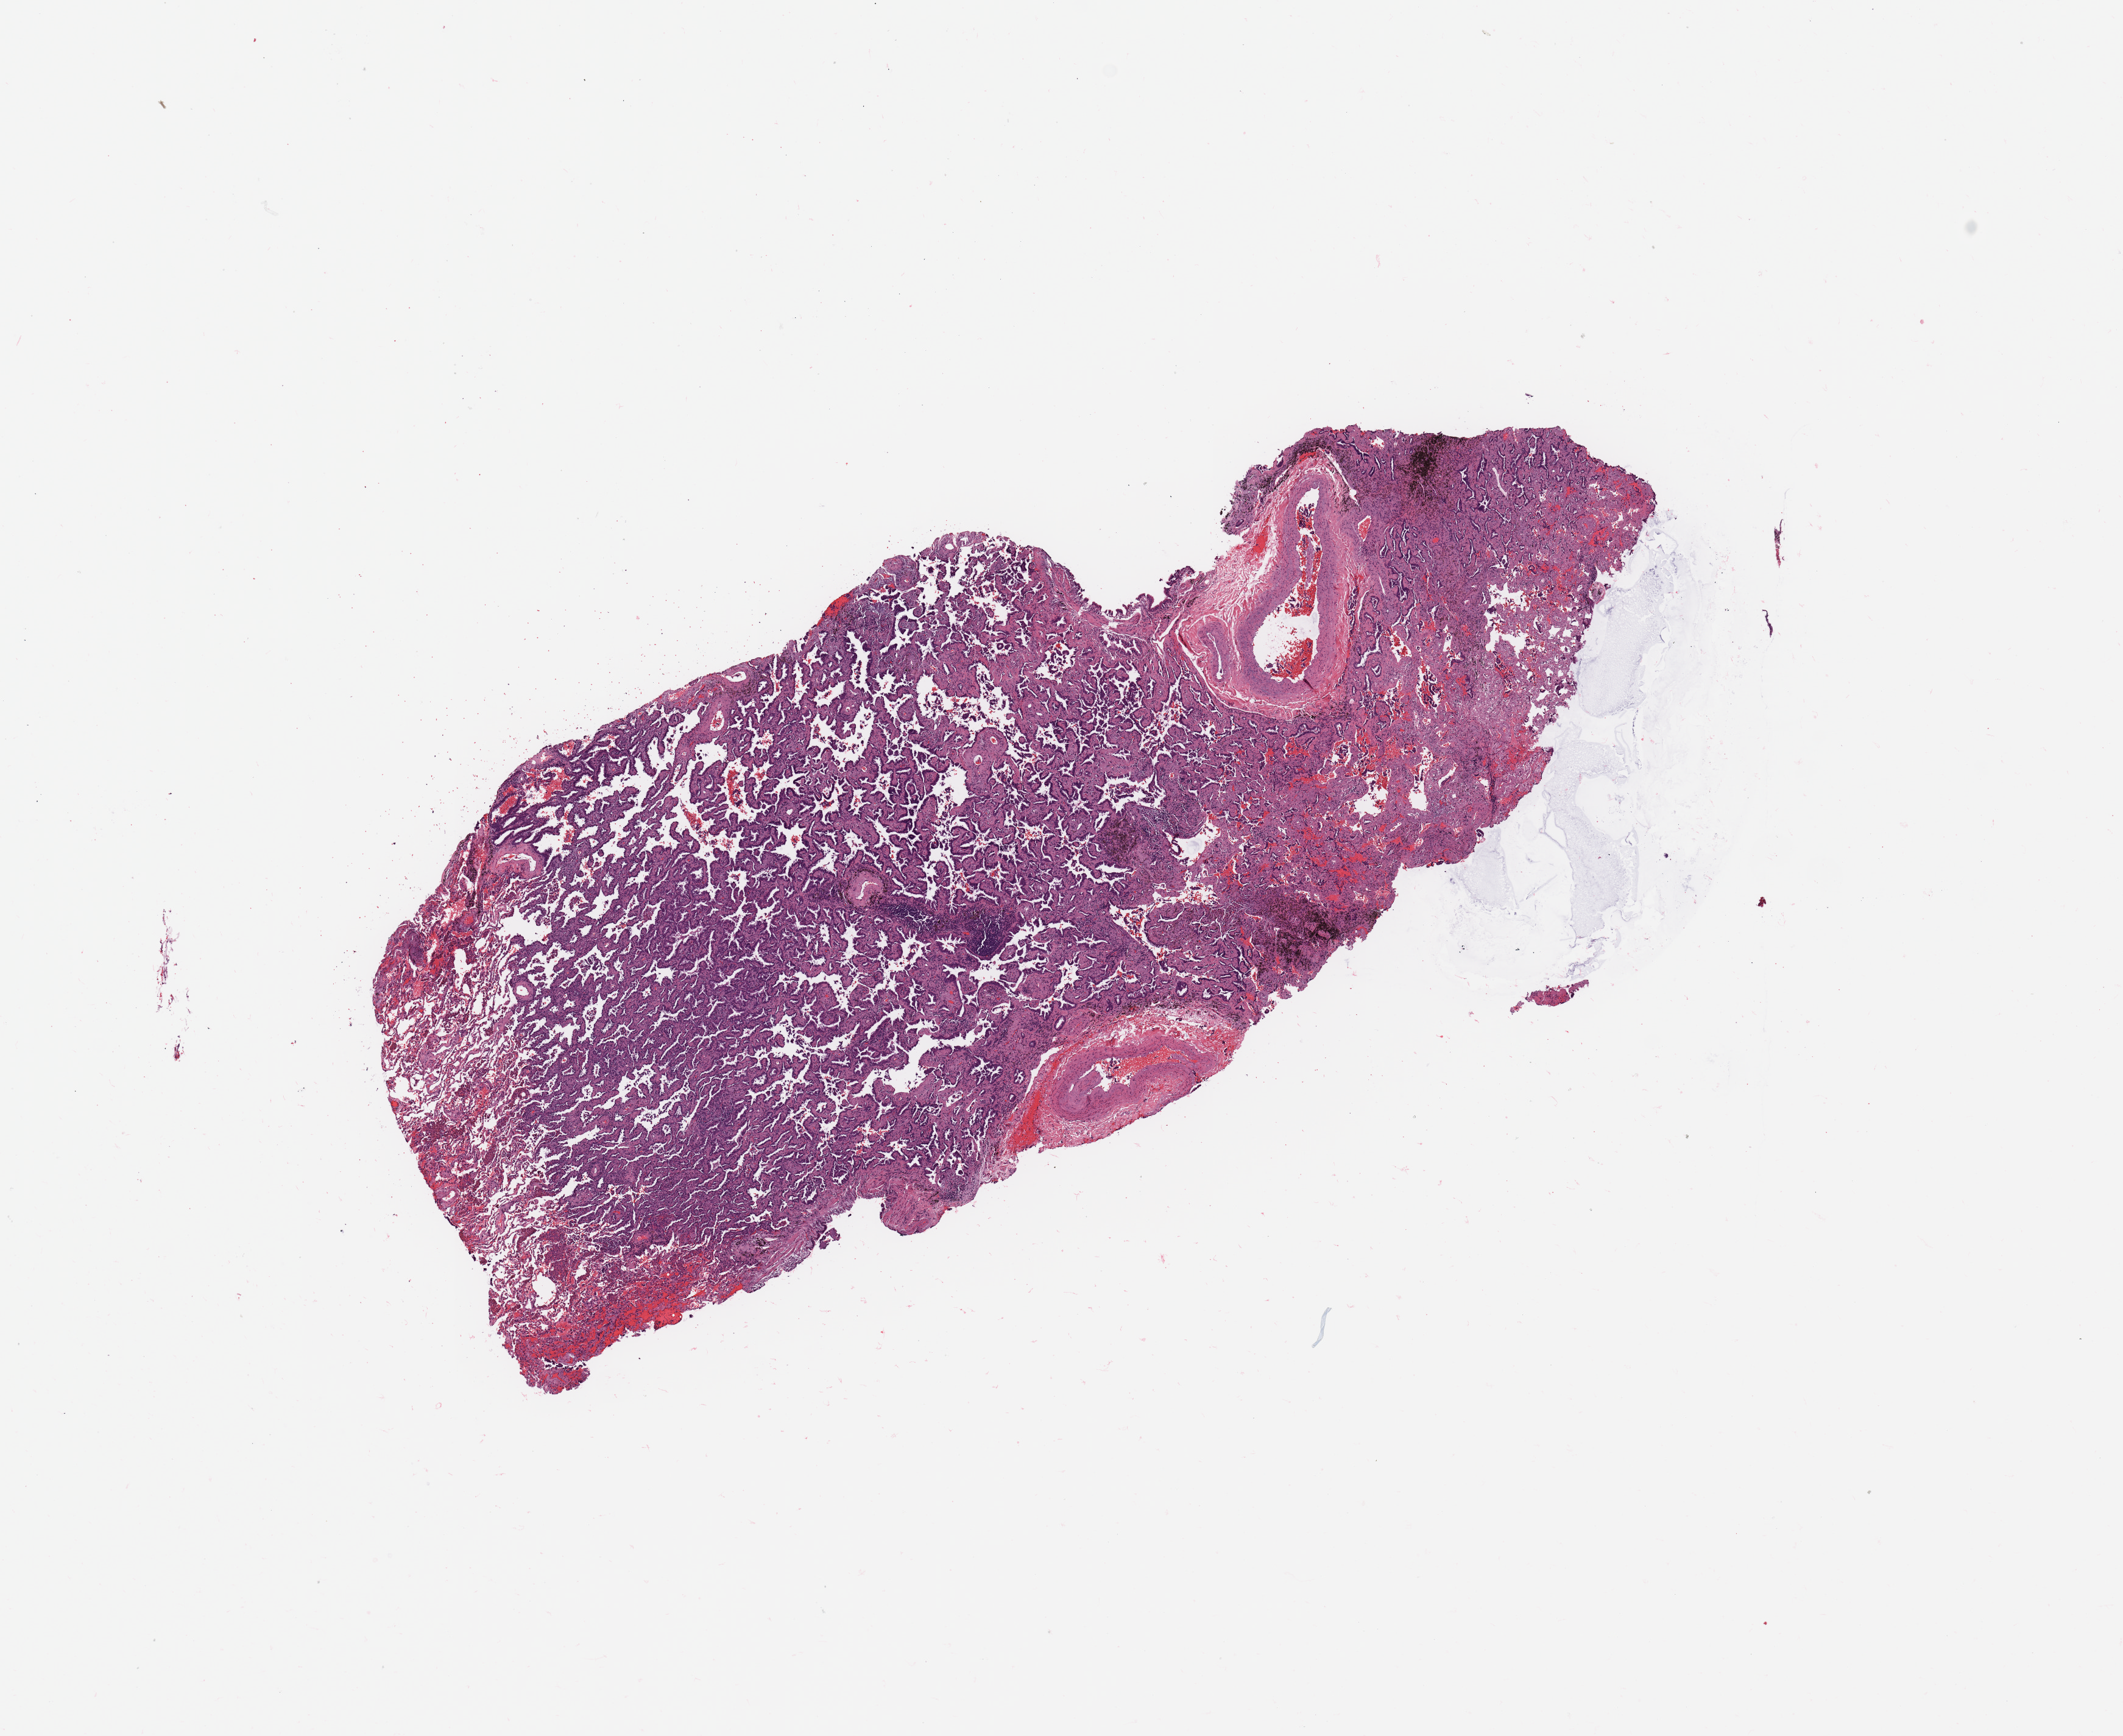
Digitized H&E-stained tissue section (whole slide), low-resolution overview of the scanned area, about 13.8 x 11.3 mm (acquisition: 20x scan), tumour tissue sample, sampled site: lung. Patient: male, age 71 years. Histologic grade: G1 (well differentiated). Pathologist review of this section (percent, as recorded): tumour nuclei 75%, necrosis 0%.
• primary tumour site (as recorded): right lower lobe
• AJCC pathologic stage: IB
• histologic diagnosis: Adenocarcinoma, NOS